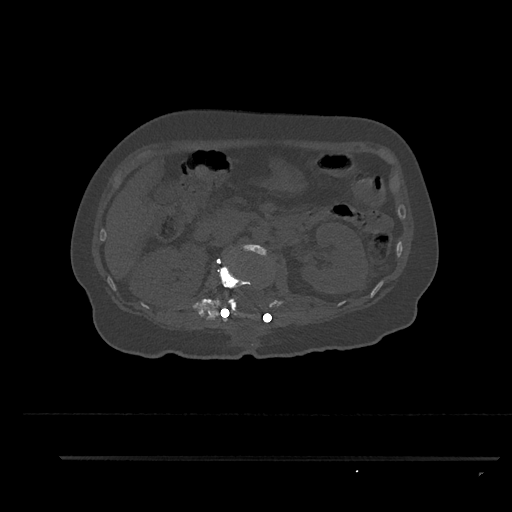
CT including the spine, one axial slice. 120 kVp. Bone window (W 1800 / L 400 HU). 512 × 512 image matrix, field of view 408 × 408 mm. Female patient, age 44 years. Case-level facts recorded for this patient, not image findings: primary cancer: renal.
Structures marked on this image (semi-automatically segmented with operator editing):
- L1 vertebra: bounding box [x1, y1, x2, y2] px = [218, 259, 251, 317]
- L2 vertebra: [226, 244, 268, 311]